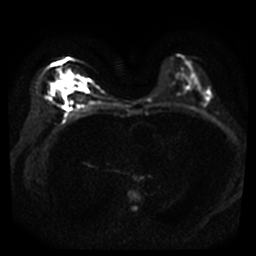
Breast MRI, one axial slice. Position 21 of 40 along the scan axis. Diffusion-weighted series; image 2 of 4 stored at this slice position (different b-values; order by instance number). 3 T. 5 mm slice thickness. 256 × 256 image matrix, field of view 320 × 320 mm. Female patient.
Structures marked on this image (outlined manually by an expert reader):
- tumour on diffusion-weighted imaging: bounding box [x1, y1, x2, y2] px = [52, 74, 74, 94]